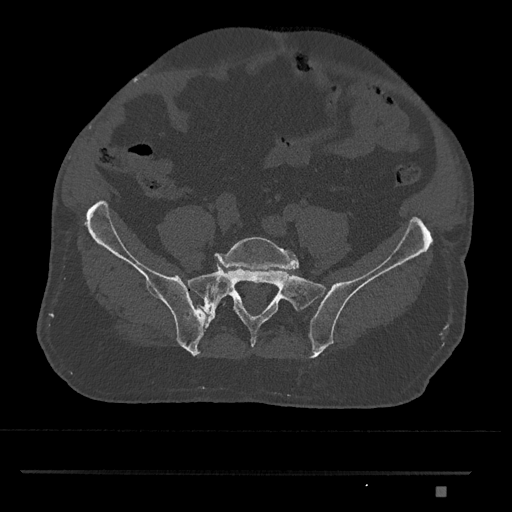
CT including the spine, one axial slice; position 519 of 1134 along the scan axis; bone window (W 1800 / L 400 HU); 0.5 mm slice thickness; 512 × 512 image matrix, field of view 429 × 429 mm. Patient: male, 65 years. From the clinical record (not read from this slice): primary cancer: prostate.
Structures marked on this image (semi-automatically segmented with operator editing):
- L5 vertebra: bounding box <214,237,299,306> (left, top, right, bottom; pixels)